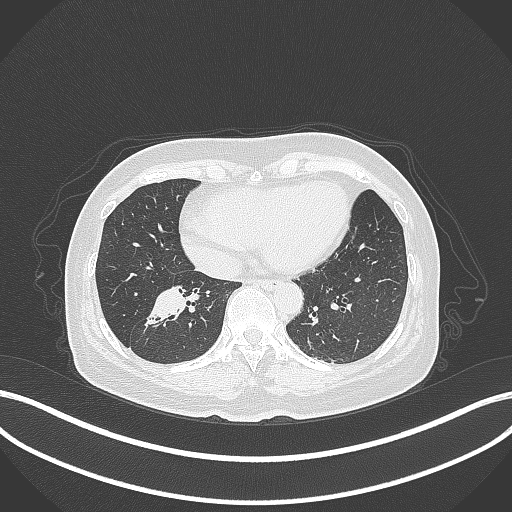
Chest CT, one axial slice. Slice 132 of 429 in the series (ordered by position). Lung window (W 1500 / L -600 HU). 1 mm slice thickness. 512 × 512 image matrix, field of view 400 × 400 mm. Patient: female, 67 years. From the clinical record (not read from this slice): clinical TNM (as recorded): T1c N1 M0.
Annotated regions visible in this slice (rectangle marked by the reading radiologist):
- lung tumour (recorded histology: adenocarcinoma): bounding box [x1, y1, x2, y2] px = [142, 282, 194, 330]